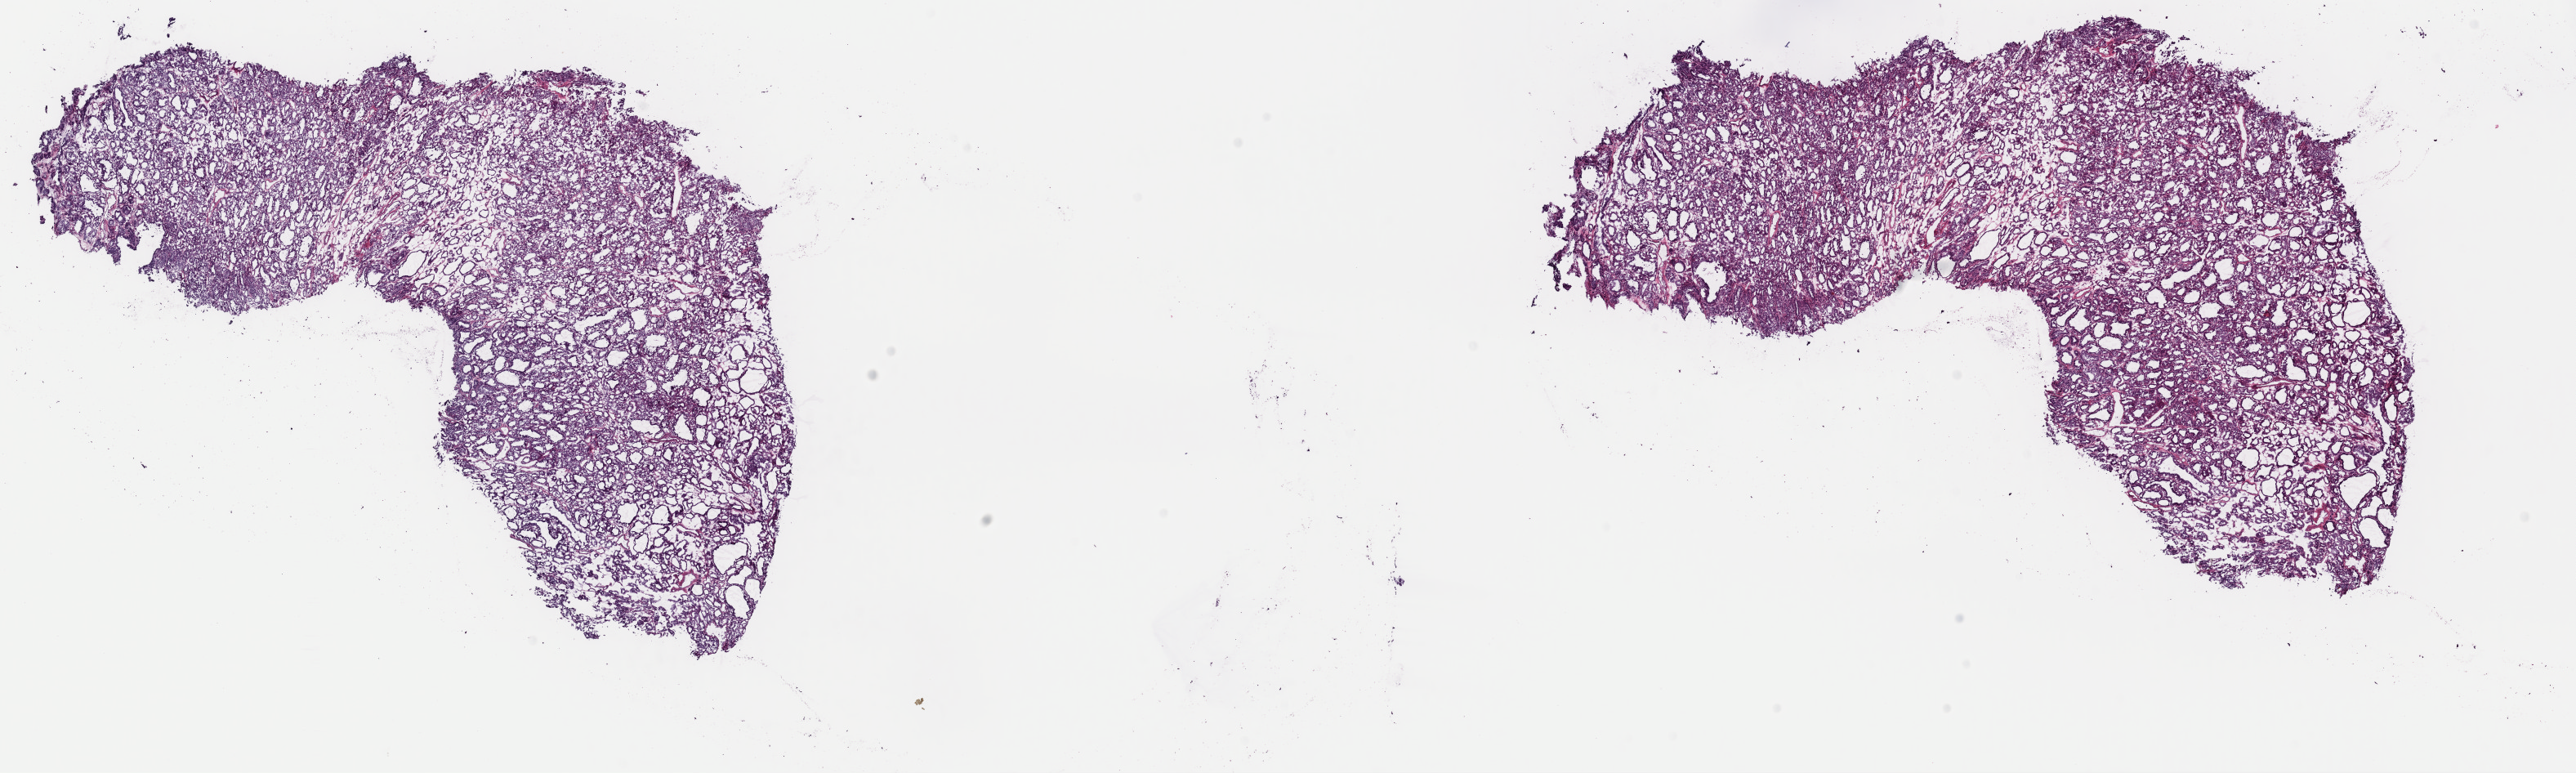
H&E whole-slide image — low-resolution overview of the scanned area, about 24.9 x 7.5 mm (slide scanned at 40x). Frozen section from the top of the tissue portion. Sample: primary tumour, thyroid. Female, age 54 years at initial diagnosis. Pathologist review of this section (percent, as recorded): tumour cells 90%, tumour nuclei 100%, normal cells 0%, stromal cells 10%, necrosis 0%. Infiltration values recorded for this section: lymphocyte infiltration 0%, monocyte infiltration 1%, neutrophil infiltration 0%.
Diagnosis: Papillary carcinoma, follicular variant (thyroid gland). AJCC pathologic stage: II (7th edition).